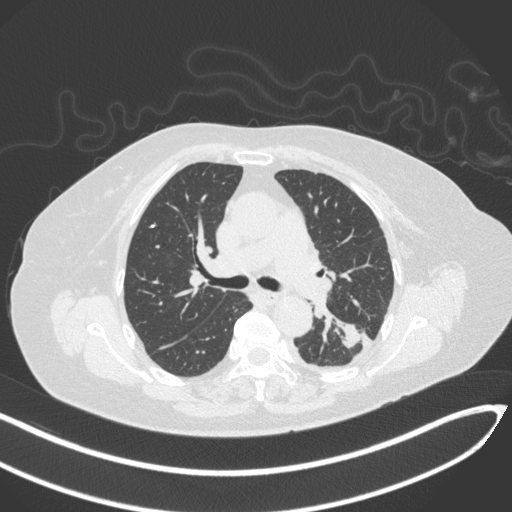
Chest CT, one axial slice; position 198 of 270 along the scan axis; reconstruction kernel B31f; lung window (W 1500 / L -600 HU); 512 × 512 image matrix, field of view 400 × 400 mm. Female patient, age 76 years. Case-level facts recorded for this patient, not image findings: clinical TNM (as recorded): T1c N0 M0.
Structures marked on this image (rectangle marked by the reading radiologist):
- lung tumour (recorded histology: adenocarcinoma): bounding box <340,318,364,350> (left, top, right, bottom; pixels)